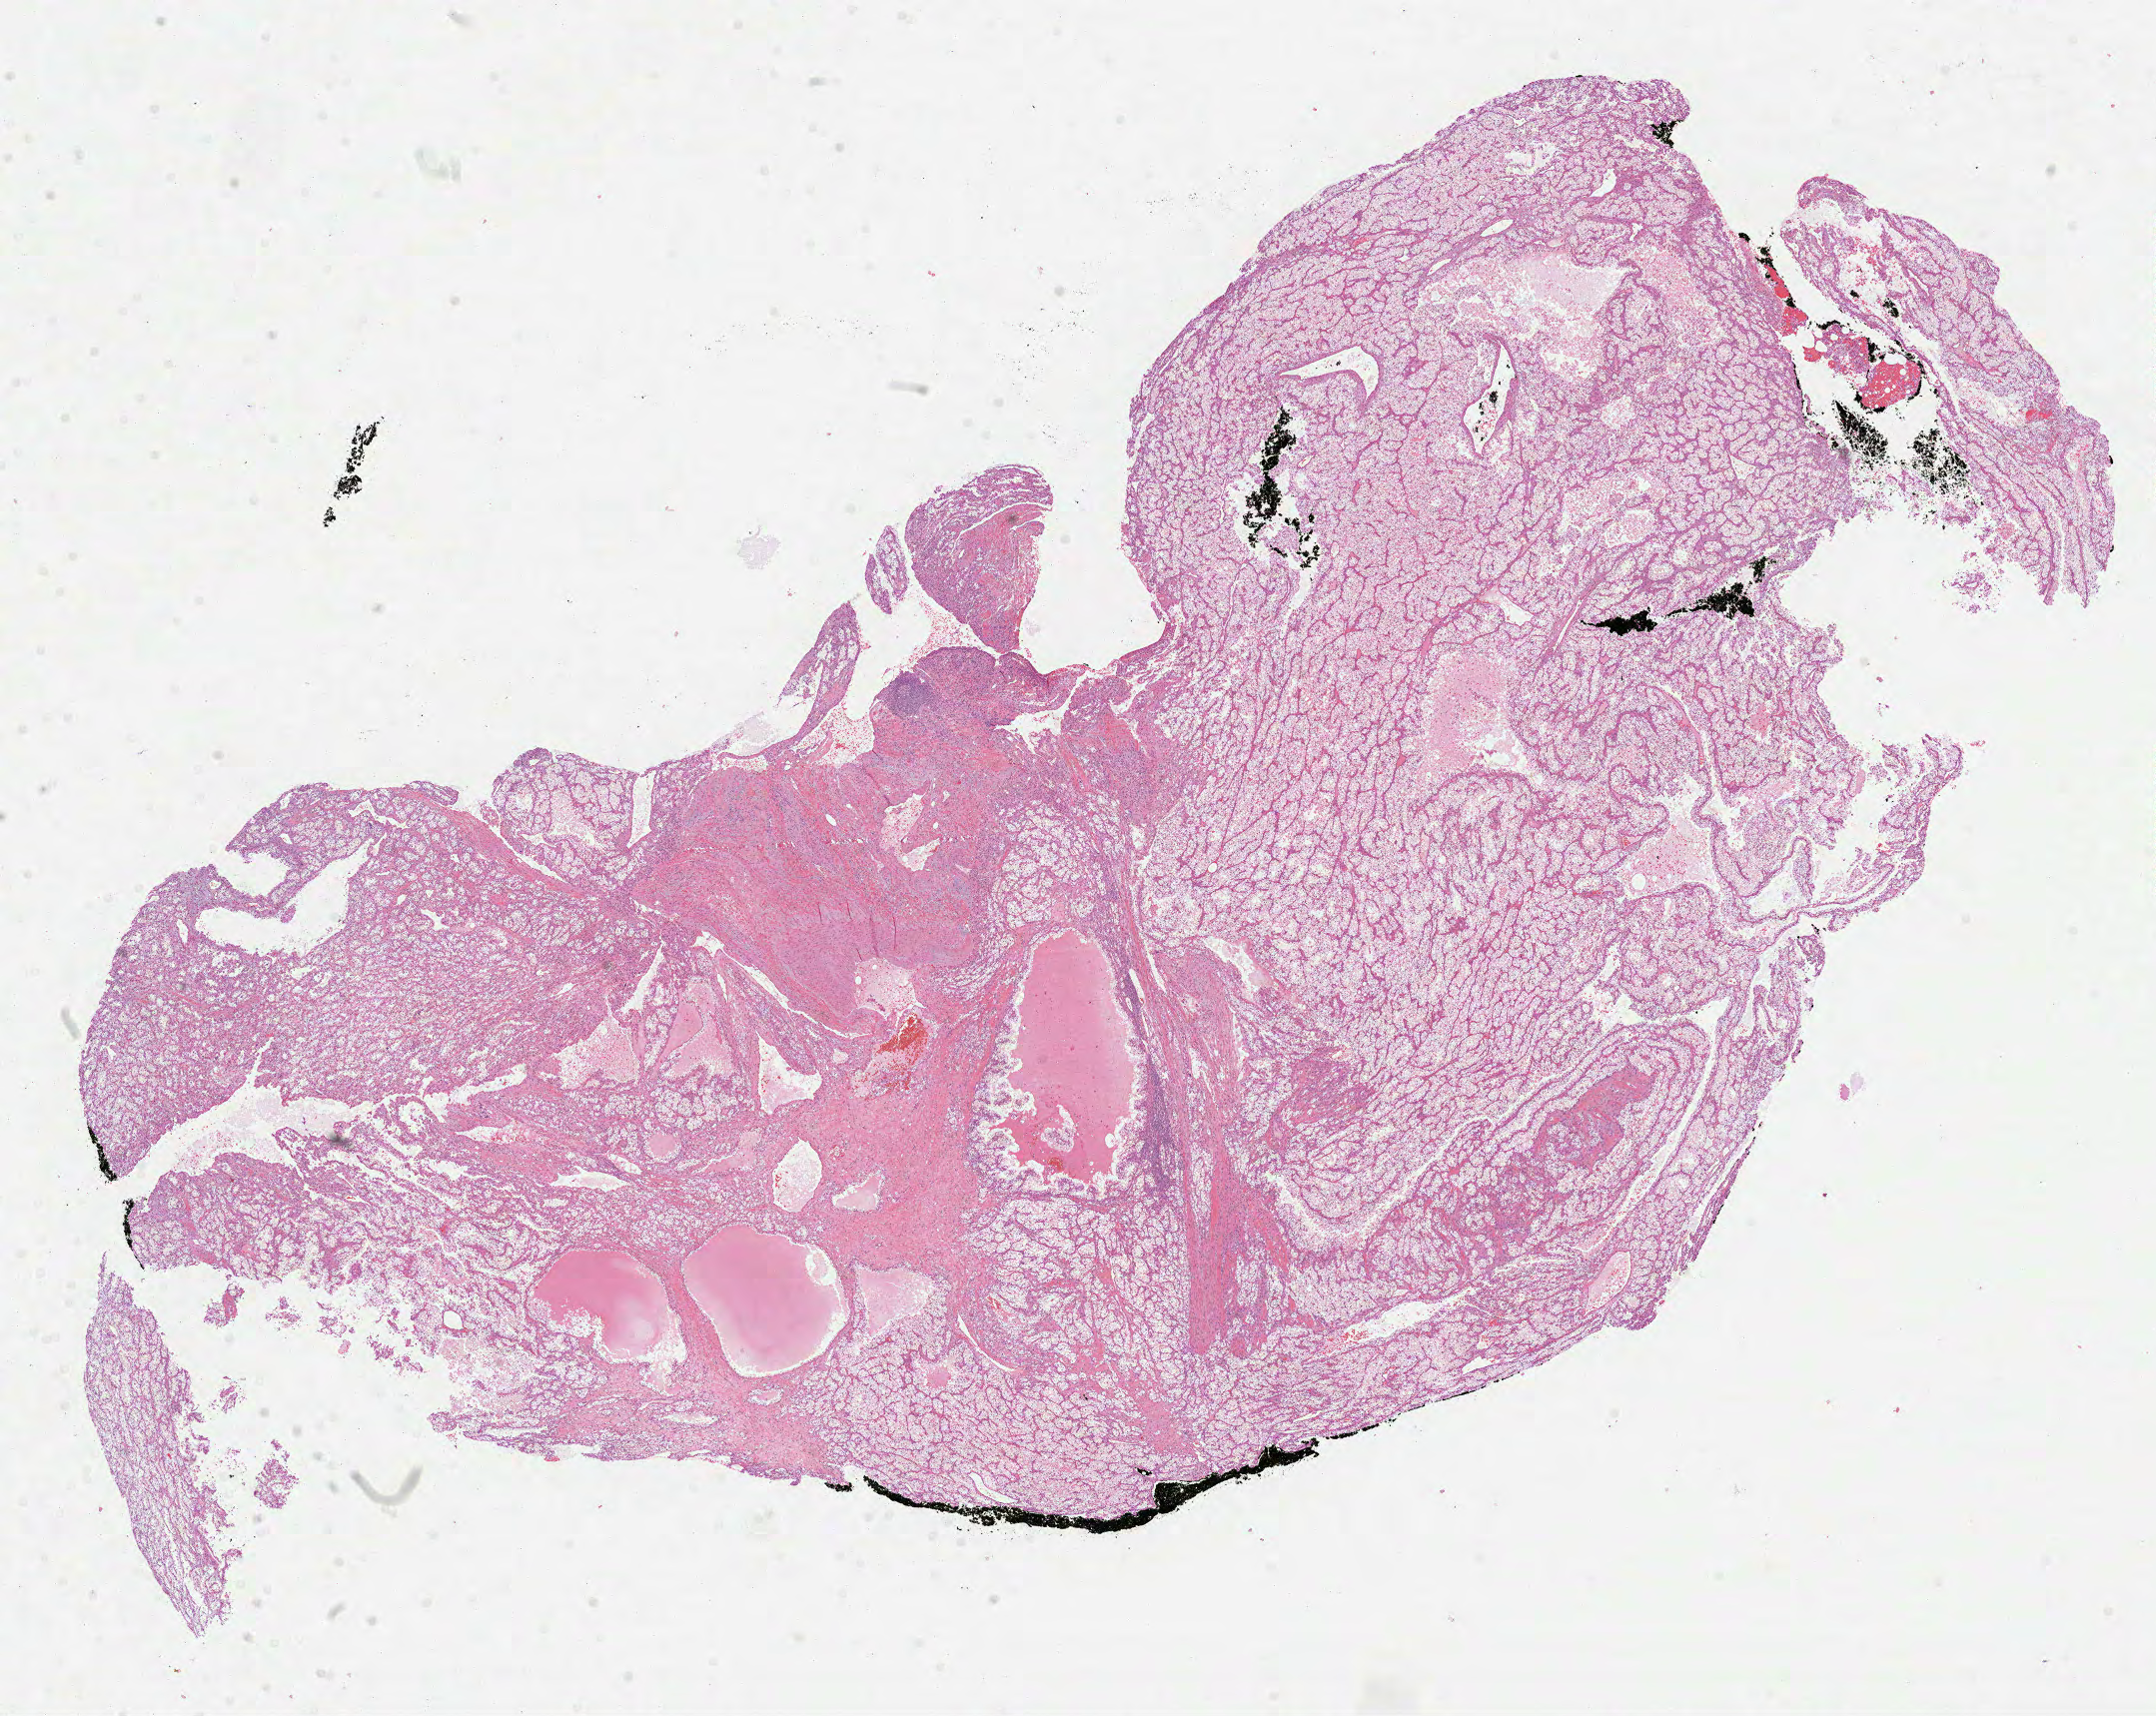
Digitized H&E tissue section (whole slide), shown as a low-resolution overview of the whole scanned area (about 17.4 x 13.9 mm, acquisition: 40x scan); FFPE section; primary tumour sample from the kidney. Patient: female, age at initial diagnosis 77 years. Histologic grade: G2 (moderately differentiated).
AJCC pathologic stage: III. Histologic diagnosis: Clear cell adenocarcinoma, NOS.